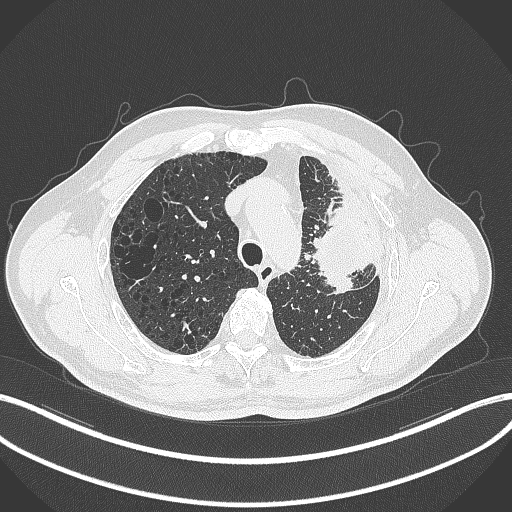
Chest CT, one axial slice. Position 244 of 297 along the scan axis. 120 kVp. Lung window (W 1500 / L -600 HU). 1 mm slice thickness. 512 × 512 image matrix. Male patient, age 68 years. Case-level facts recorded for this patient, not image findings: clinical TNM (as recorded): T3 N3 M1.
Structures marked on this image (bounding box drawn by a radiologist):
- lung tumour (recorded histology: adenocarcinoma): bounding box [x1, y1, x2, y2] px = [307, 190, 369, 298]